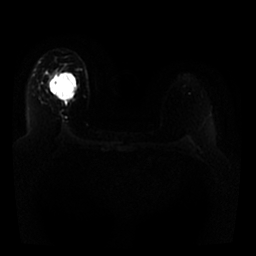
Breast MRI, one axial slice; diffusion-weighted series; image 2 of 4 stored at this slice position (different b-values; order by instance number); 1.5 T; 4 mm slice thickness; 256 × 256 image matrix. Female patient.
Annotated regions visible in this slice (manually delineated by an expert):
- tumour on diffusion-weighted imaging: bounding box (x1, y1, x2, y2) in pixels: (48, 73, 57, 85)